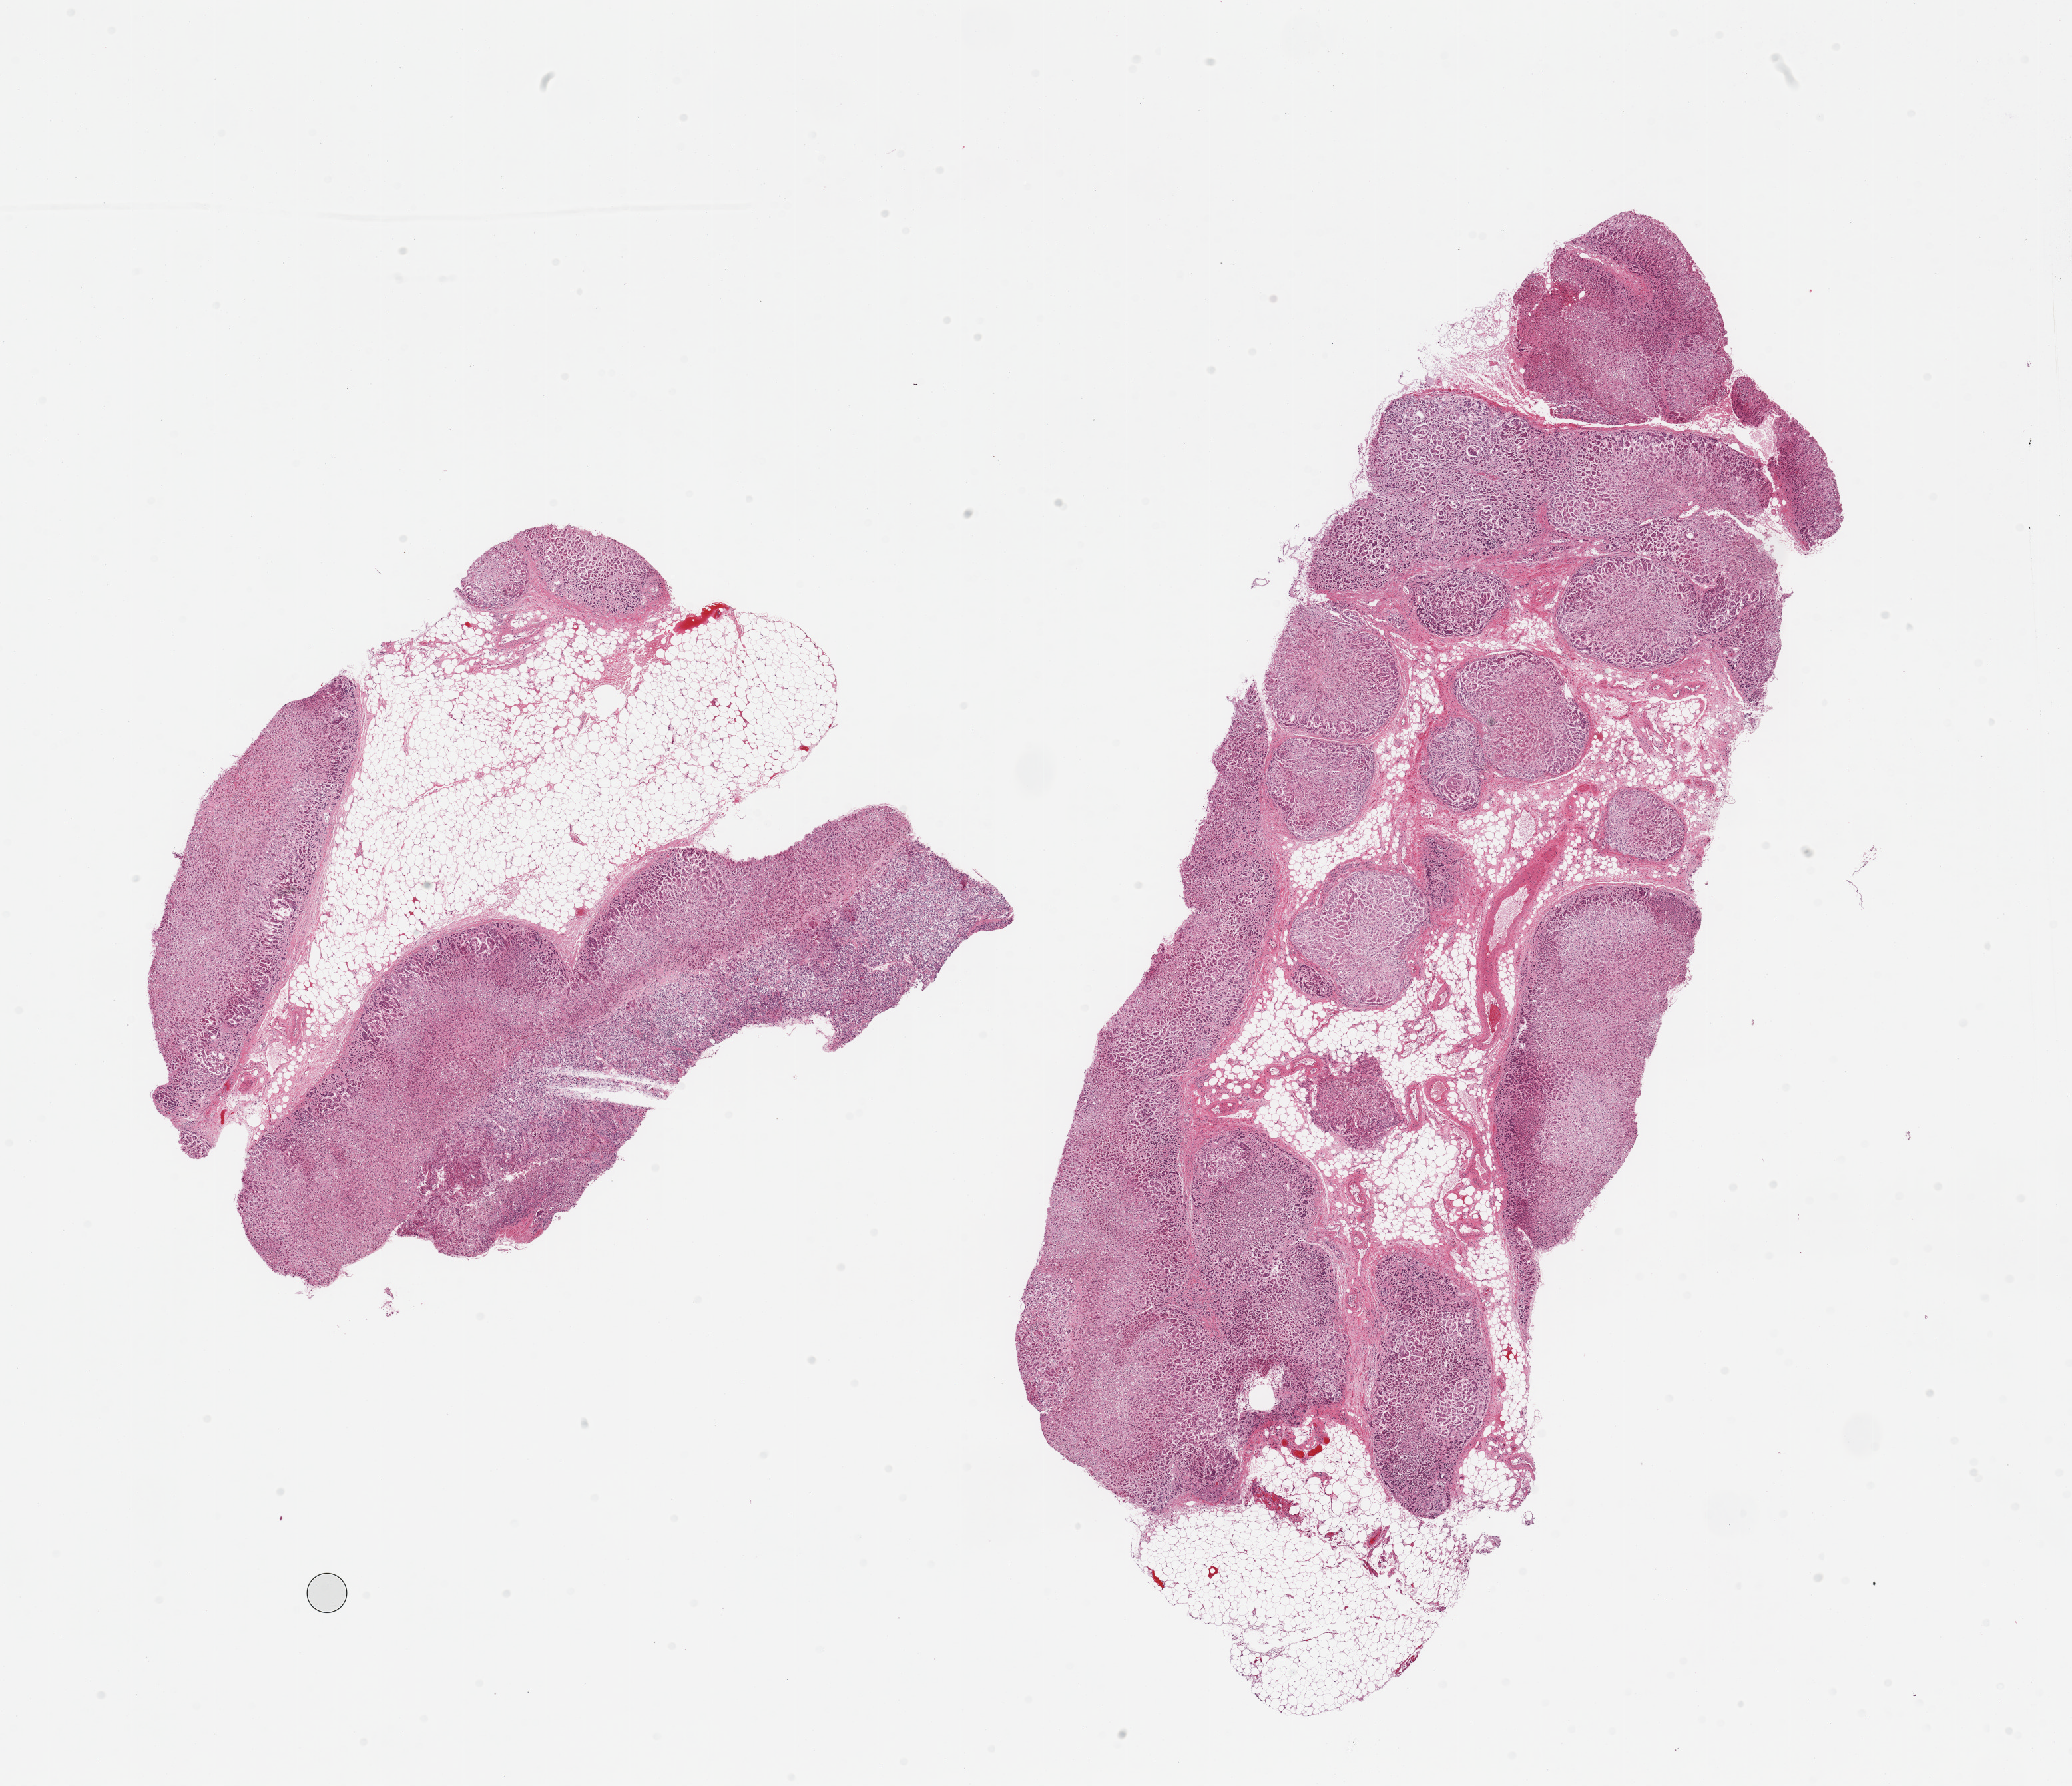
Whole-slide image, H&E stain, low-resolution overview of the scanned area, about 24.6 x 21.2 mm, PAXgene-fixed paraffin-embedded (PFPE) section, target tissue: adrenal gland, tissue donor sample. Donor sex: male.
Review note (as recorded): 2 pieces, all cortex, moderate autolysis; adherent fat is ~10-15% specimen.